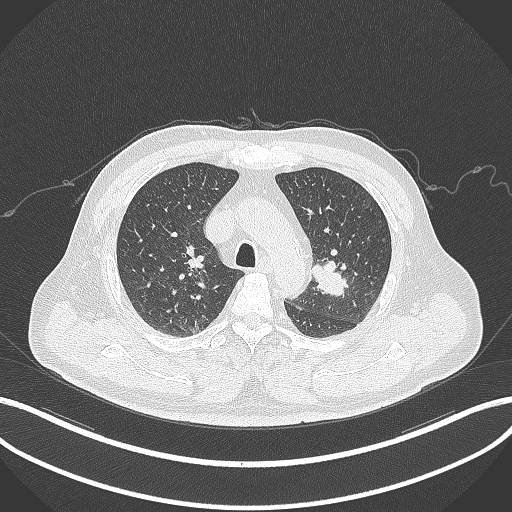
Chest CT, one axial slice. Reconstruction kernel B70f. Lung window (W 1500 / L -600 HU). 1 mm slice thickness. 512 × 512 image matrix. Patient: male, 67 years. Case-level facts recorded for this patient, not image findings: clinical TNM (as recorded): T2a N1 M0.
Structures marked on this image (bounding box drawn by a radiologist):
- lung tumour (recorded histology: adenocarcinoma): bounding box [x1, y1, x2, y2] px = [305, 255, 352, 299]